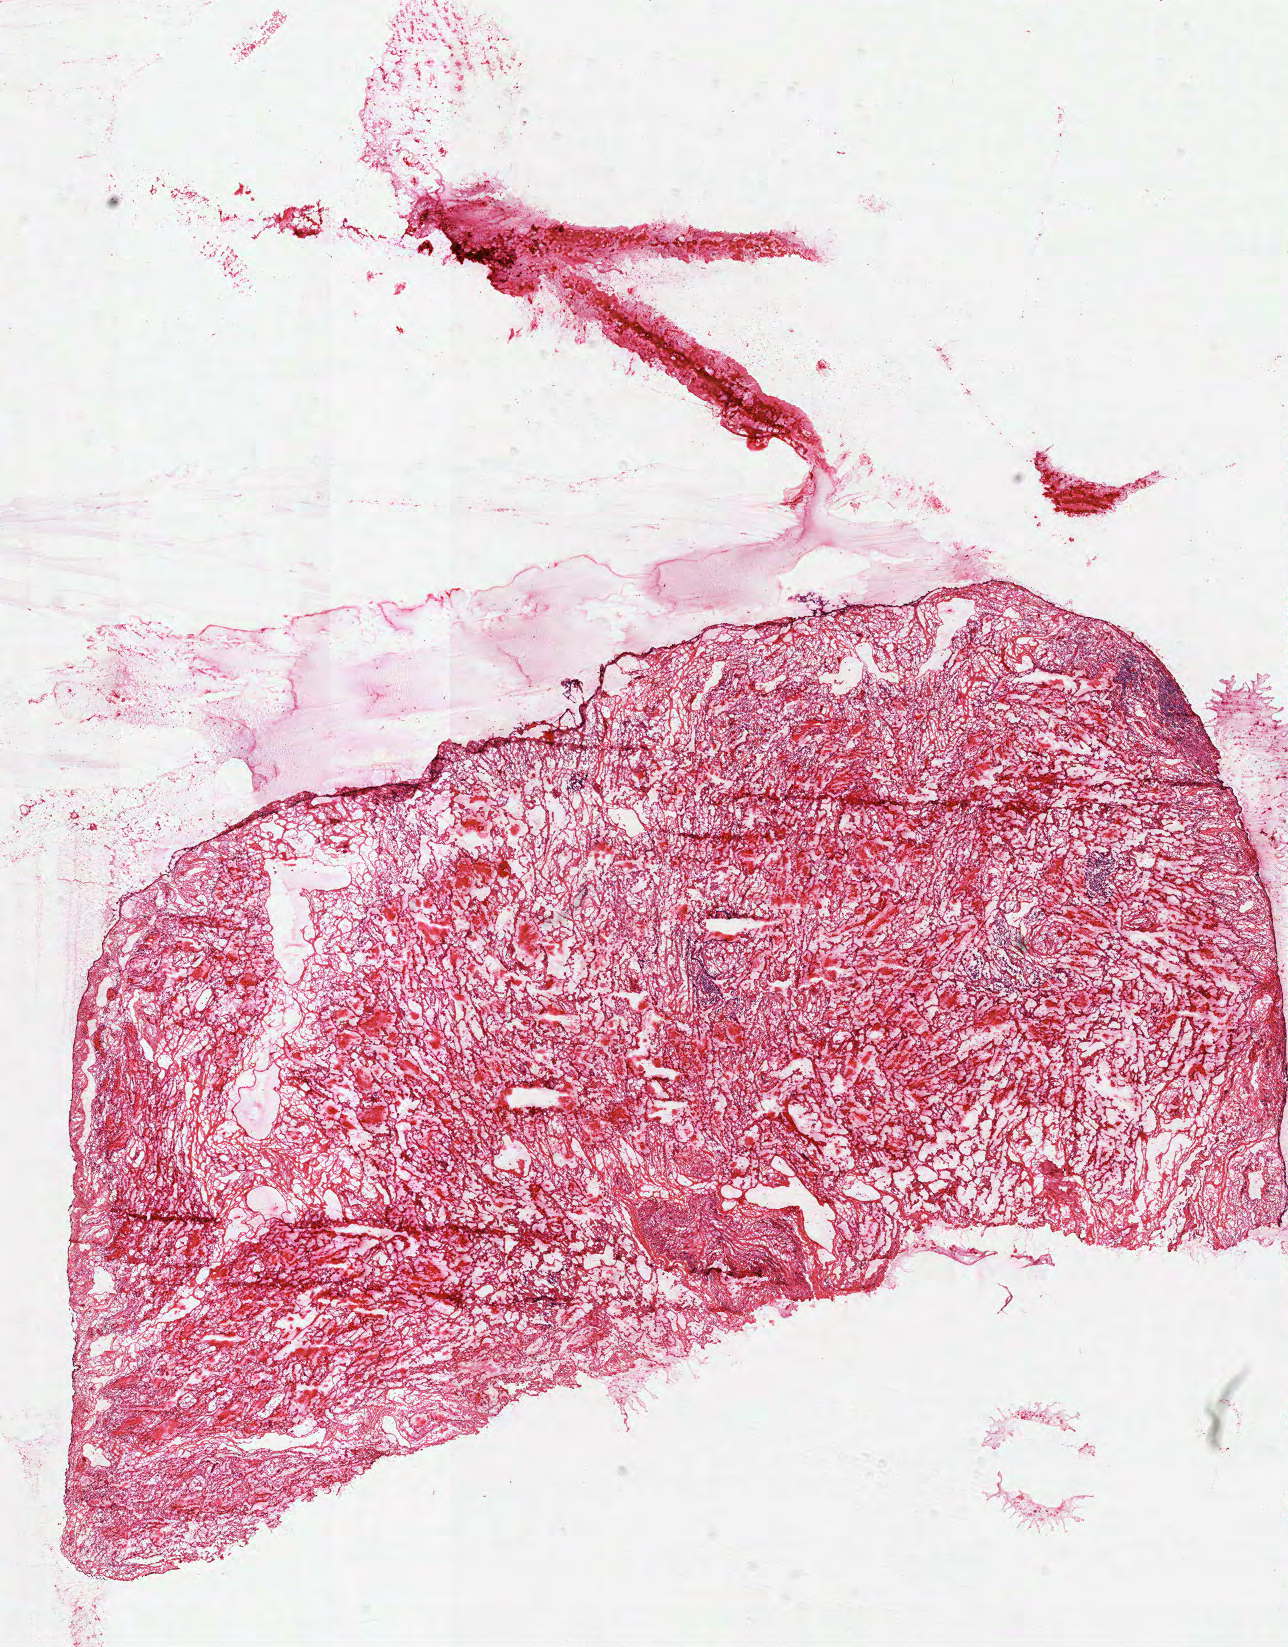
H&E whole-slide image — a low-resolution overview of the entire scanned area, about 10.4 x 13.3 mm (from a 40x scan), frozen section from the top of the tissue portion, sample: solid tissue normal (non-tumour tissue), lung. Patient: male, age at initial diagnosis 67 years.
This section: solid tissue normal (non-tumour) sample from the same patient. Patient diagnosis: Squamous cell carcinoma, NOS (upper lobe, lung).